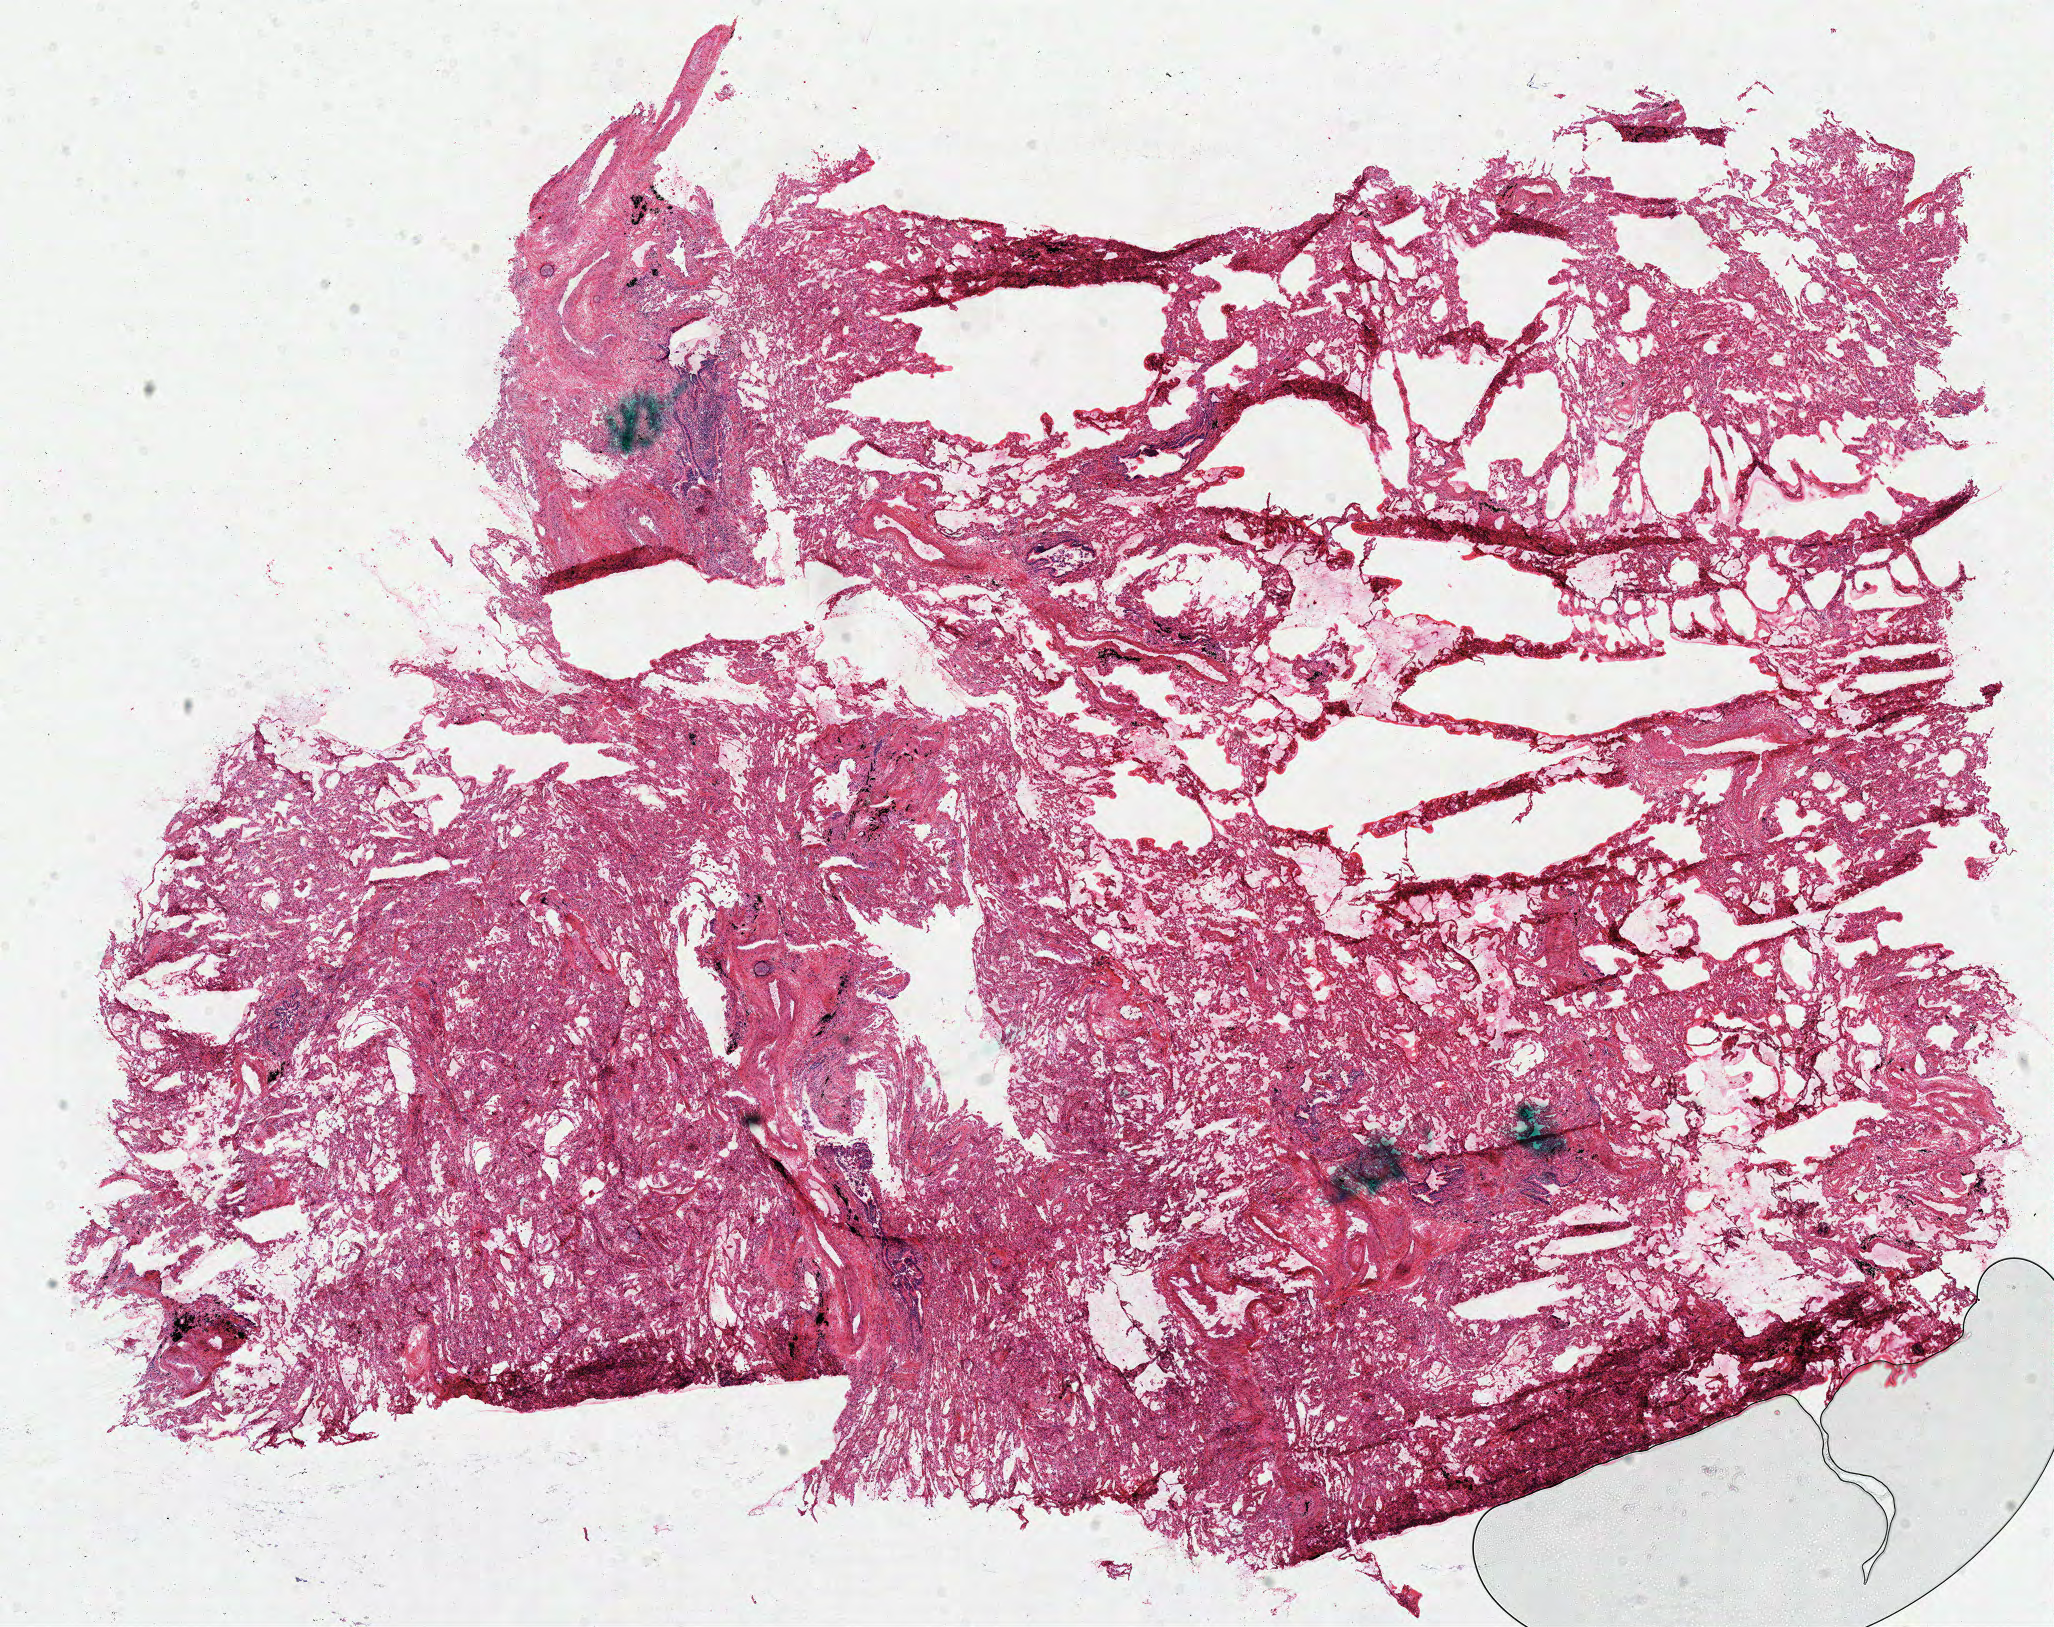
Whole-slide histology image, H&E-stained — a low-resolution overview of the entire scanned area, about 16.2 x 12.8 mm (from a 40x scan). Frozen section from the top of the tissue portion. Sample: solid tissue normal (non-tumour tissue), lung. Patient: male, age at initial diagnosis 72 years.
This section: solid tissue normal sample (biorepository sample class). Patient diagnosis: Adenocarcinoma, NOS (lower lobe, lung).